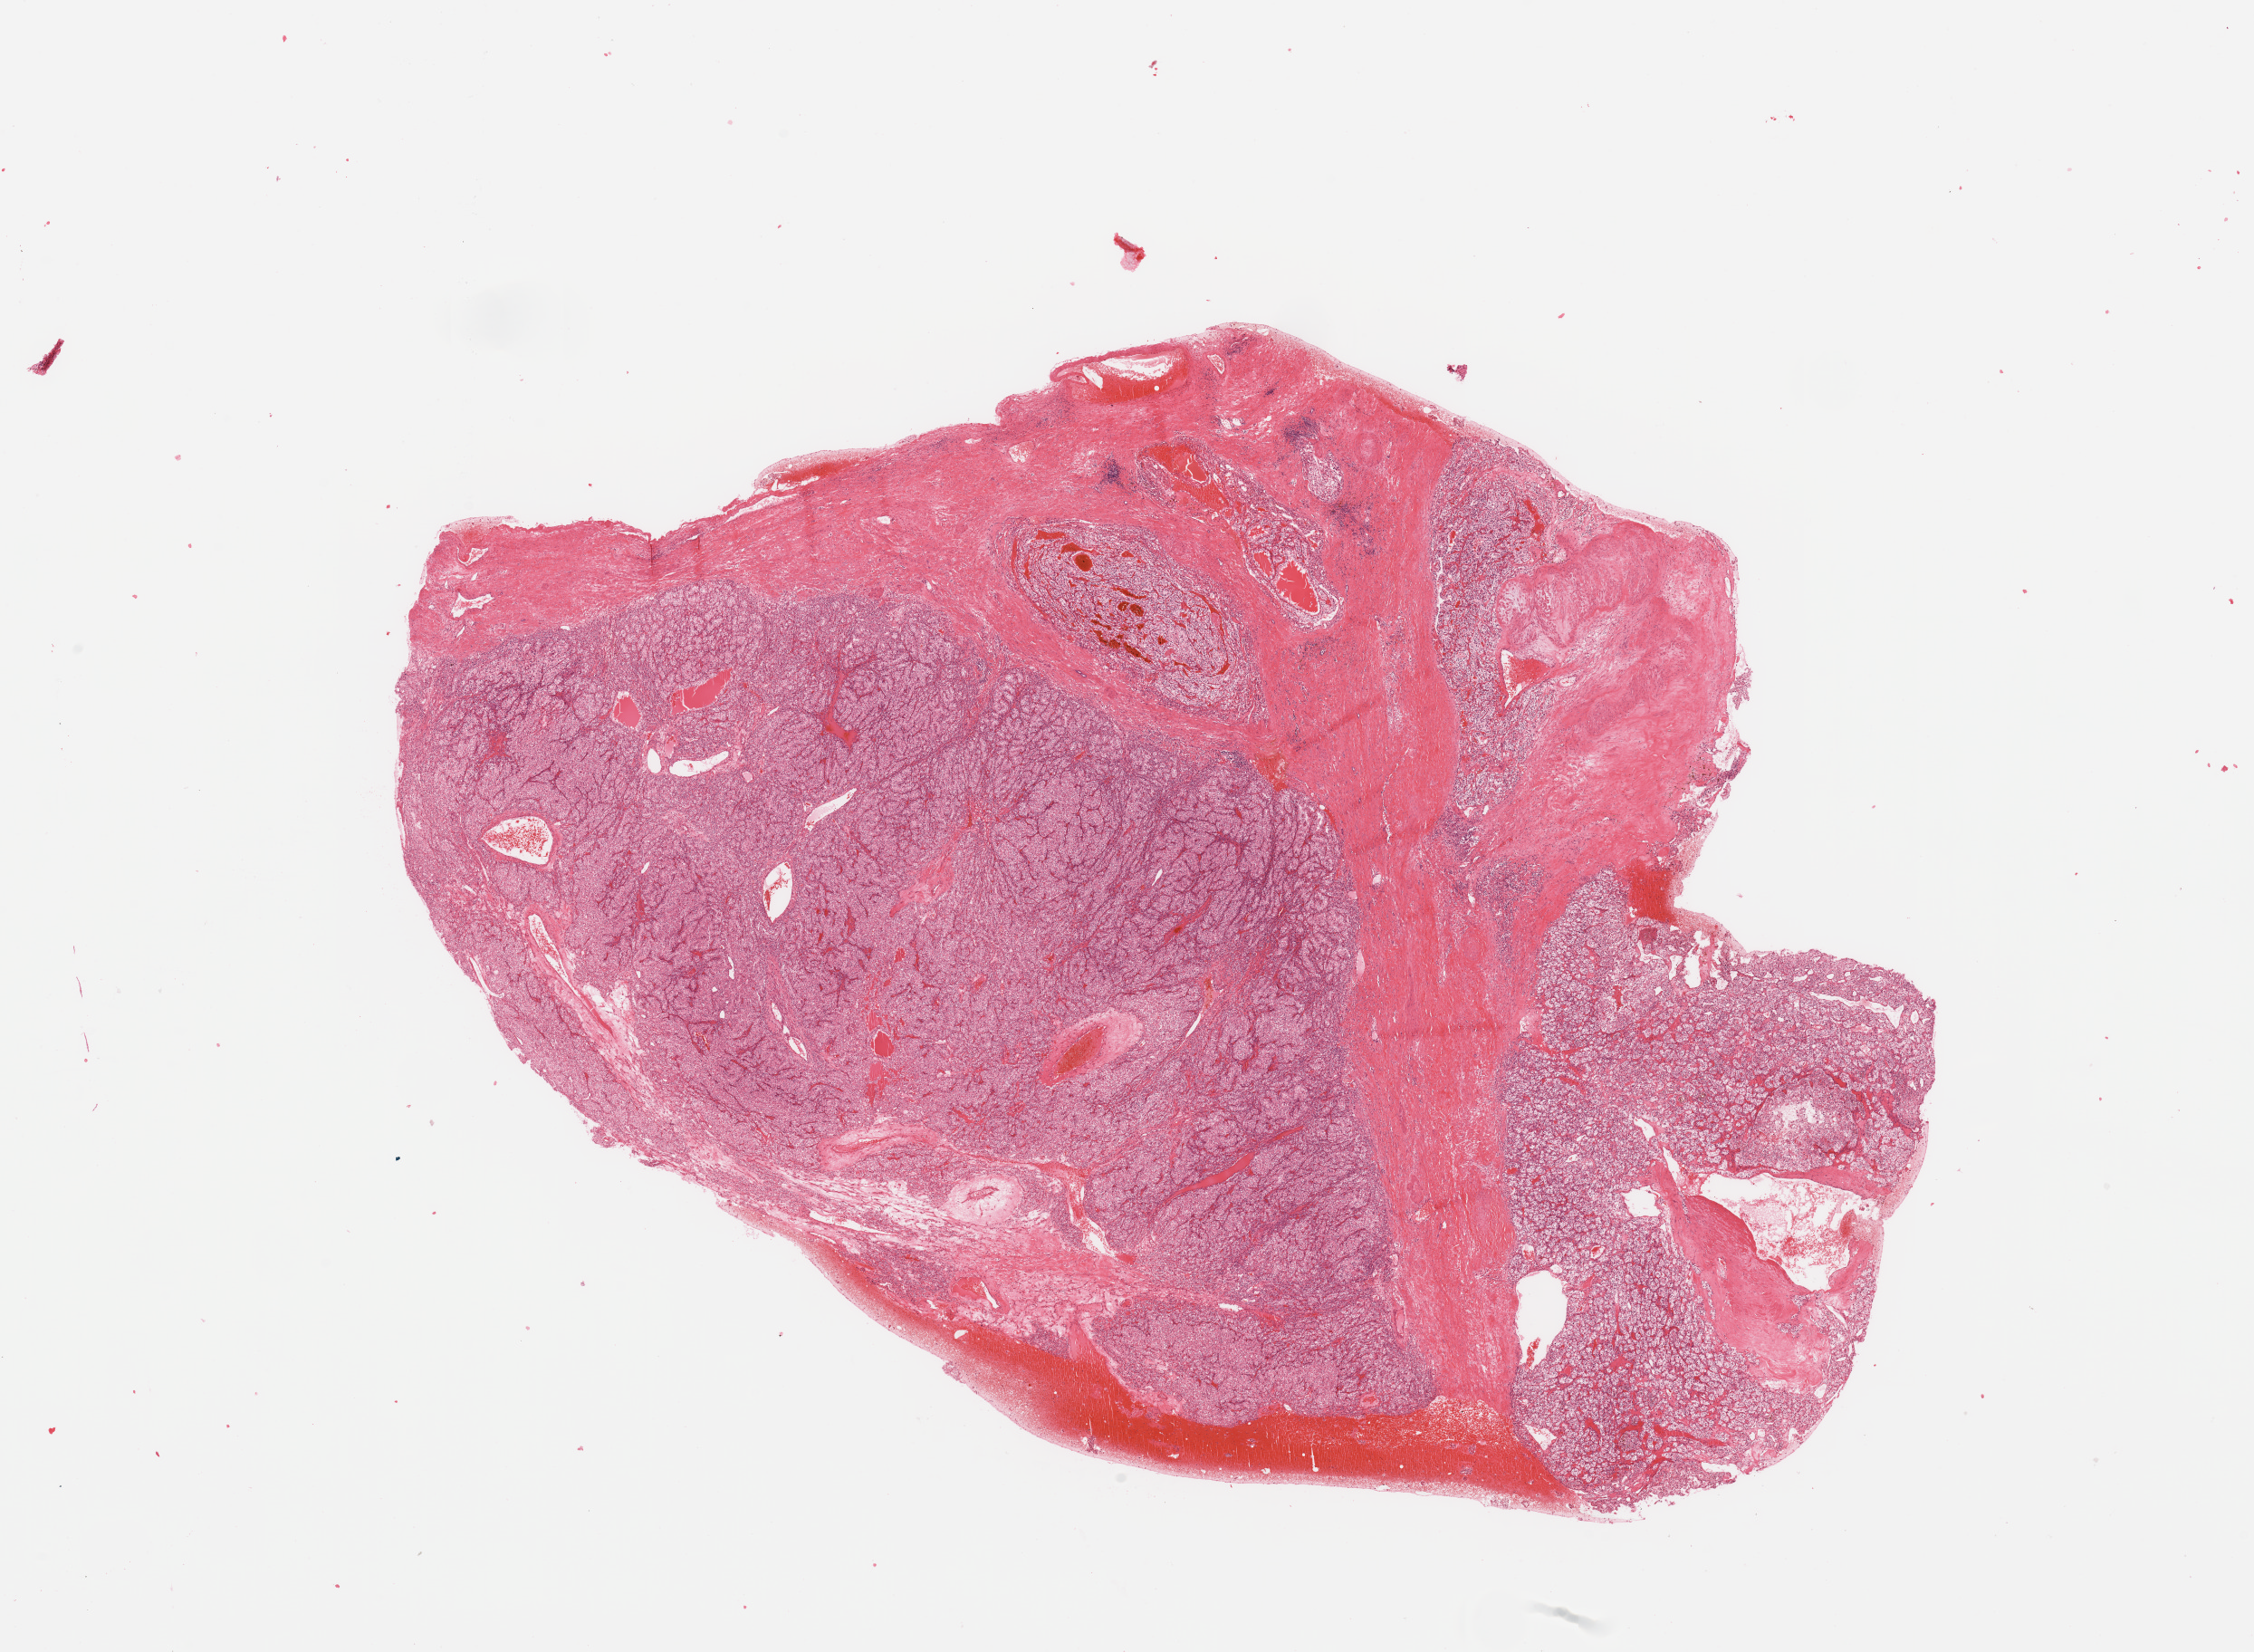
Digitized Hematoxylin and eosin (H&E) stained tissue section (whole slide), whole scanned area (about 19.7 x 14.4 mm, acquisition: 20x scan) shown as a low-resolution overview, tumour tissue sample, sampled site: kidney. 61-year-old male patient. Histologic grade: G2 (moderately differentiated). Composition of this section per pathologist review: tumour nuclei 85%, necrosis 10%.
AJCC pathologic stage: II. Diagnosis: Renal cell carcinoma, NOS.